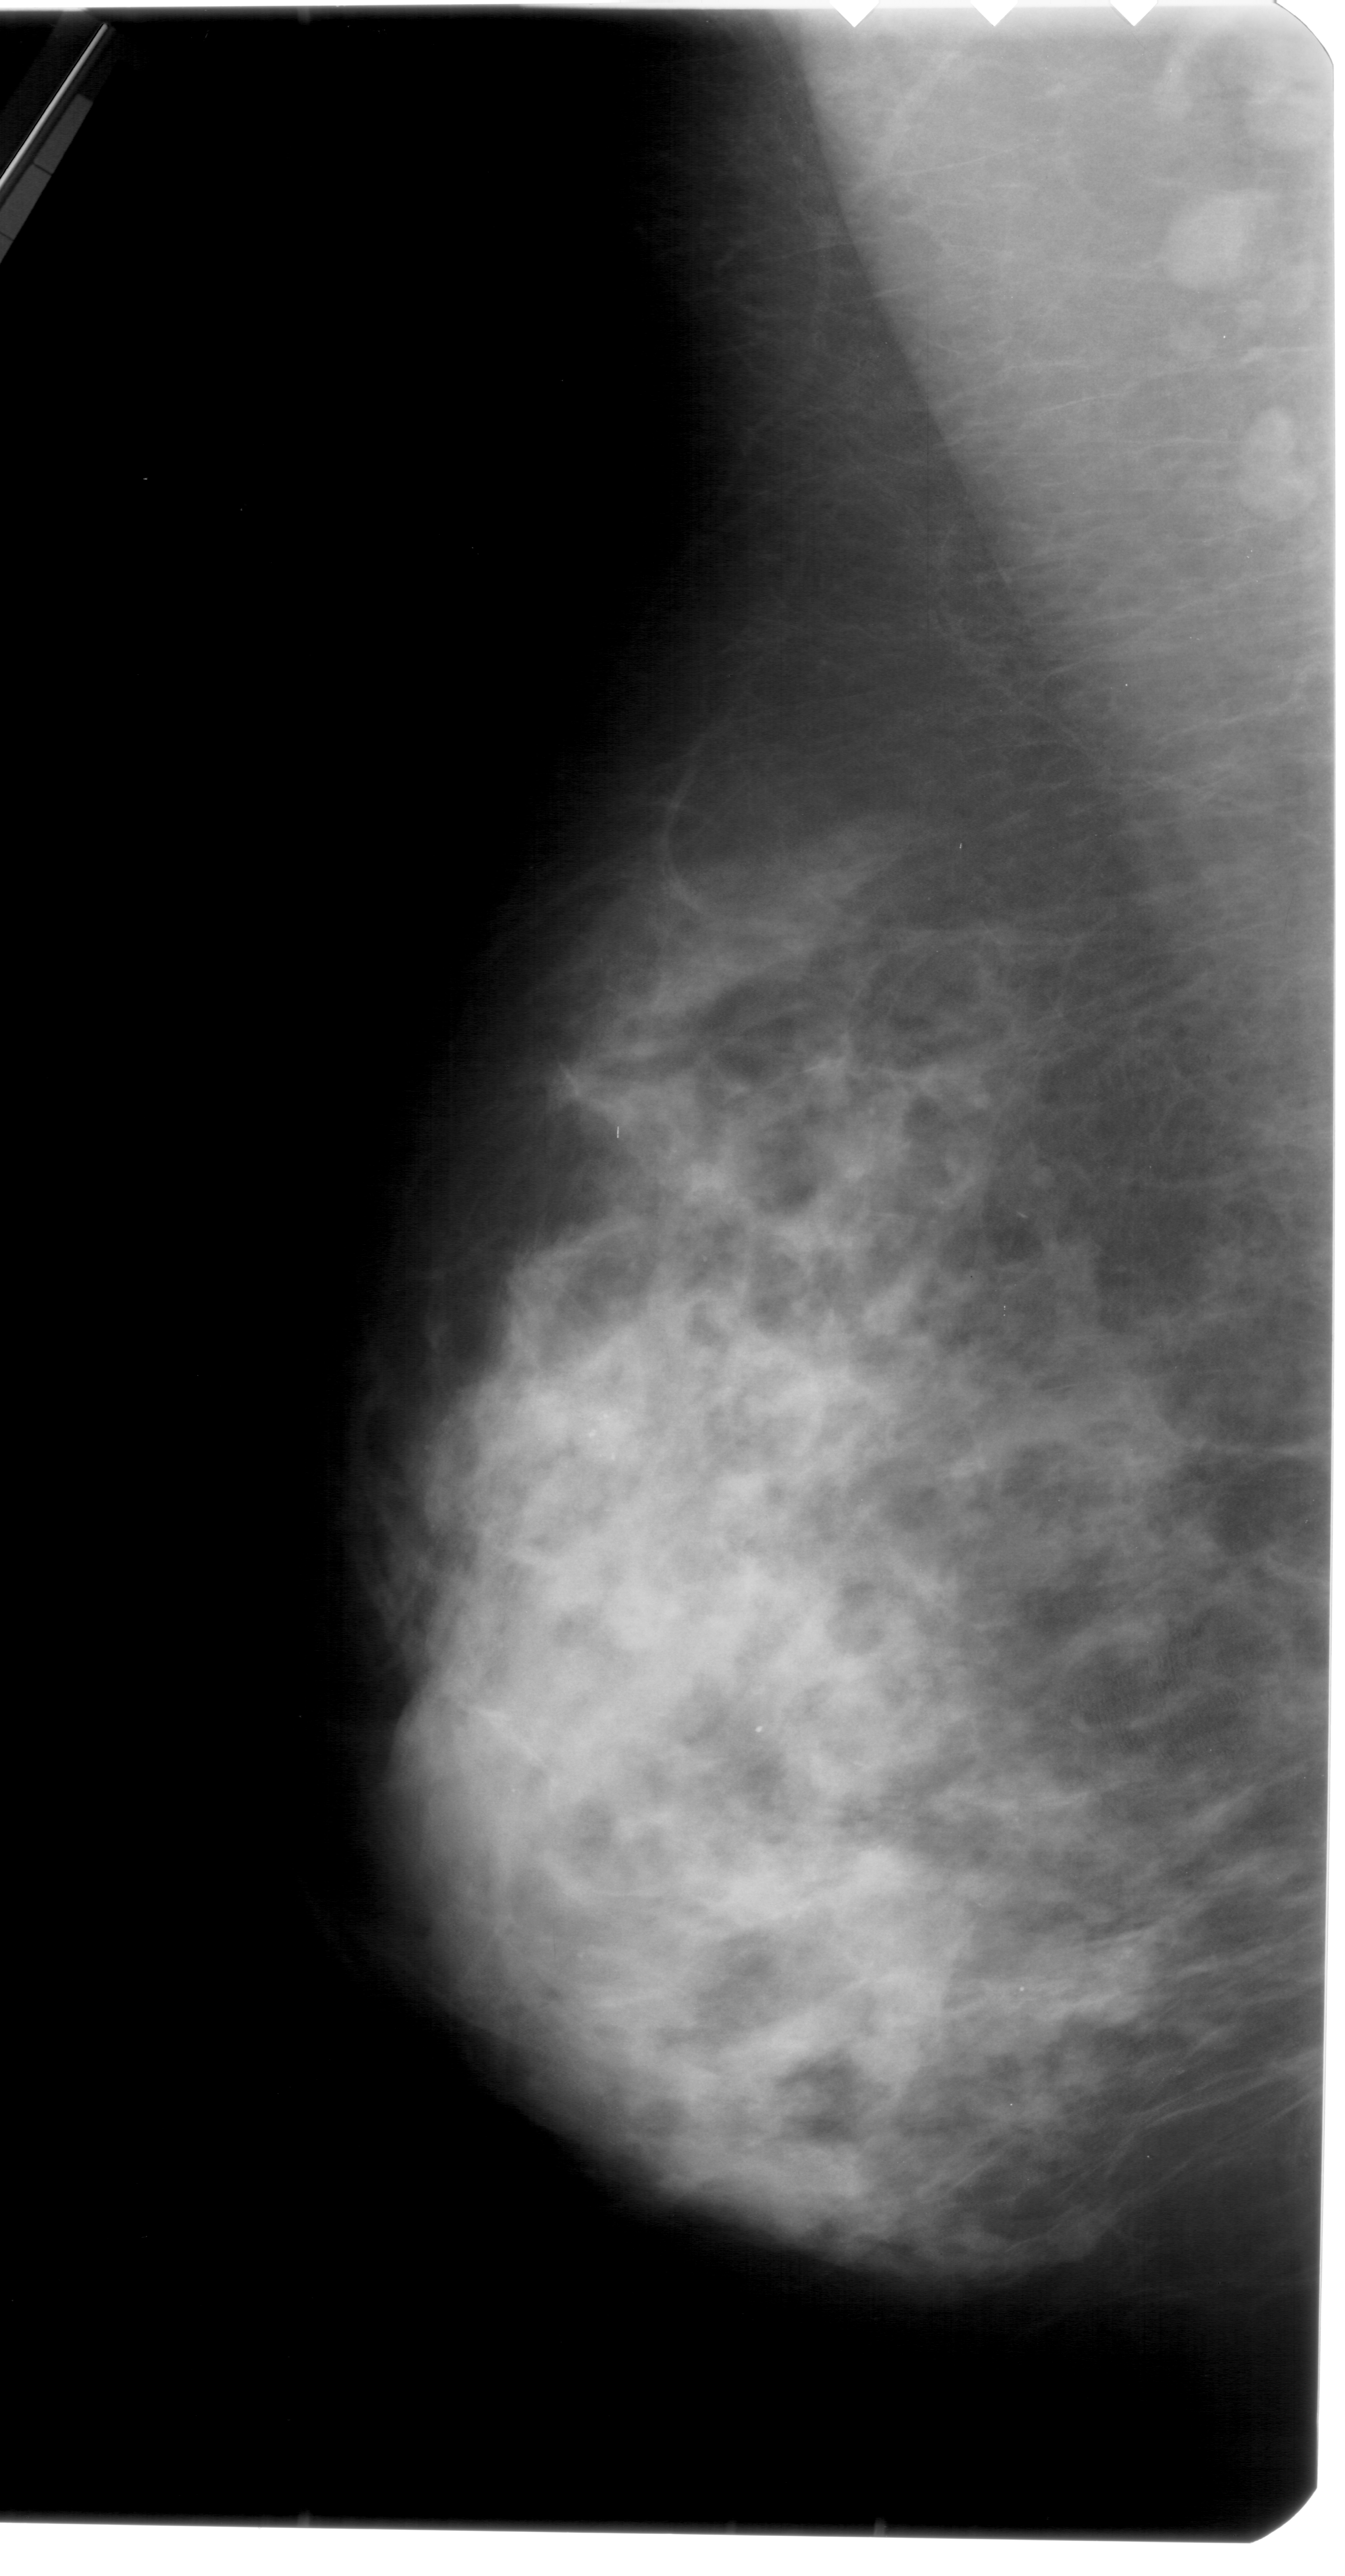
Mammogram (digitized film). Left breast. Mediolateral oblique (MLO) view. BI-RADS breast density category 4 (scale 1–4). 1345 × 2576 image matrix.
Expert-marked regions of interest on this image (one box per marked abnormality):
- calcifications, morphology pleomorphic, distribution clustered; BI-RADS assessment category 4; pathology result (as recorded, not read from the image): malignant: bounding box <484,1315,718,1542> (left, top, right, bottom; pixels)